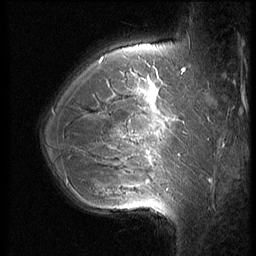
Breast MRI (dynamic contrast-enhanced), one sagittal slice; 3 images stored at this slice position (order not interpretable as contrast timing); 1.5 T; TE 4.2 ms, TR 9 ms; 256 × 256 image matrix, field of view 180 × 180 mm. Patient: female, 35 years. Case-level facts recorded for this patient, not image findings: setting: breast cancer imaged before/during neoadjuvant chemotherapy; receptor status: HR-positive, HER2-negative.
Annotated regions visible in this slice (semi-automatically segmented with operator editing):
- analysis volume of interest (the breast-tissue region the enhancement analysis was run in; not a lesion): bounding box [x1, y1, x2, y2] px = [63, 60, 190, 218]
- tumour enhancement mask (voxels above the 140 % enhancement threshold inside the analysis volume of interest): [114, 91, 174, 191]